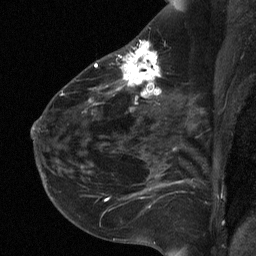
Breast MRI (dynamic contrast-enhanced), one sagittal slice. Position 40 of 64 along the scan axis. Dynamic contrast-enhanced study with each time point stored as its own series, time point 2 of 3 at this slice position (early post-contrast, ordered by acquisition time). 1.5 T. TE 4.8 ms, TR 27 ms. 256 × 256 image matrix. Patient: female, 51 years. Case-level facts recorded for this patient, not image findings: setting: breast cancer imaged before/during neoadjuvant chemotherapy; receptor status: HR-positive, HER2-negative.
Annotated regions visible in this slice (semi-automatically segmented with operator editing):
- analysis volume of interest (the breast-tissue region the enhancement analysis was run in; not a lesion): box from (x=72, y=34) to (x=182, y=118) px
- tumour enhancement mask (voxels above the 90 % enhancement threshold inside the analysis volume of interest): (x=95, y=41)–(x=161, y=104)